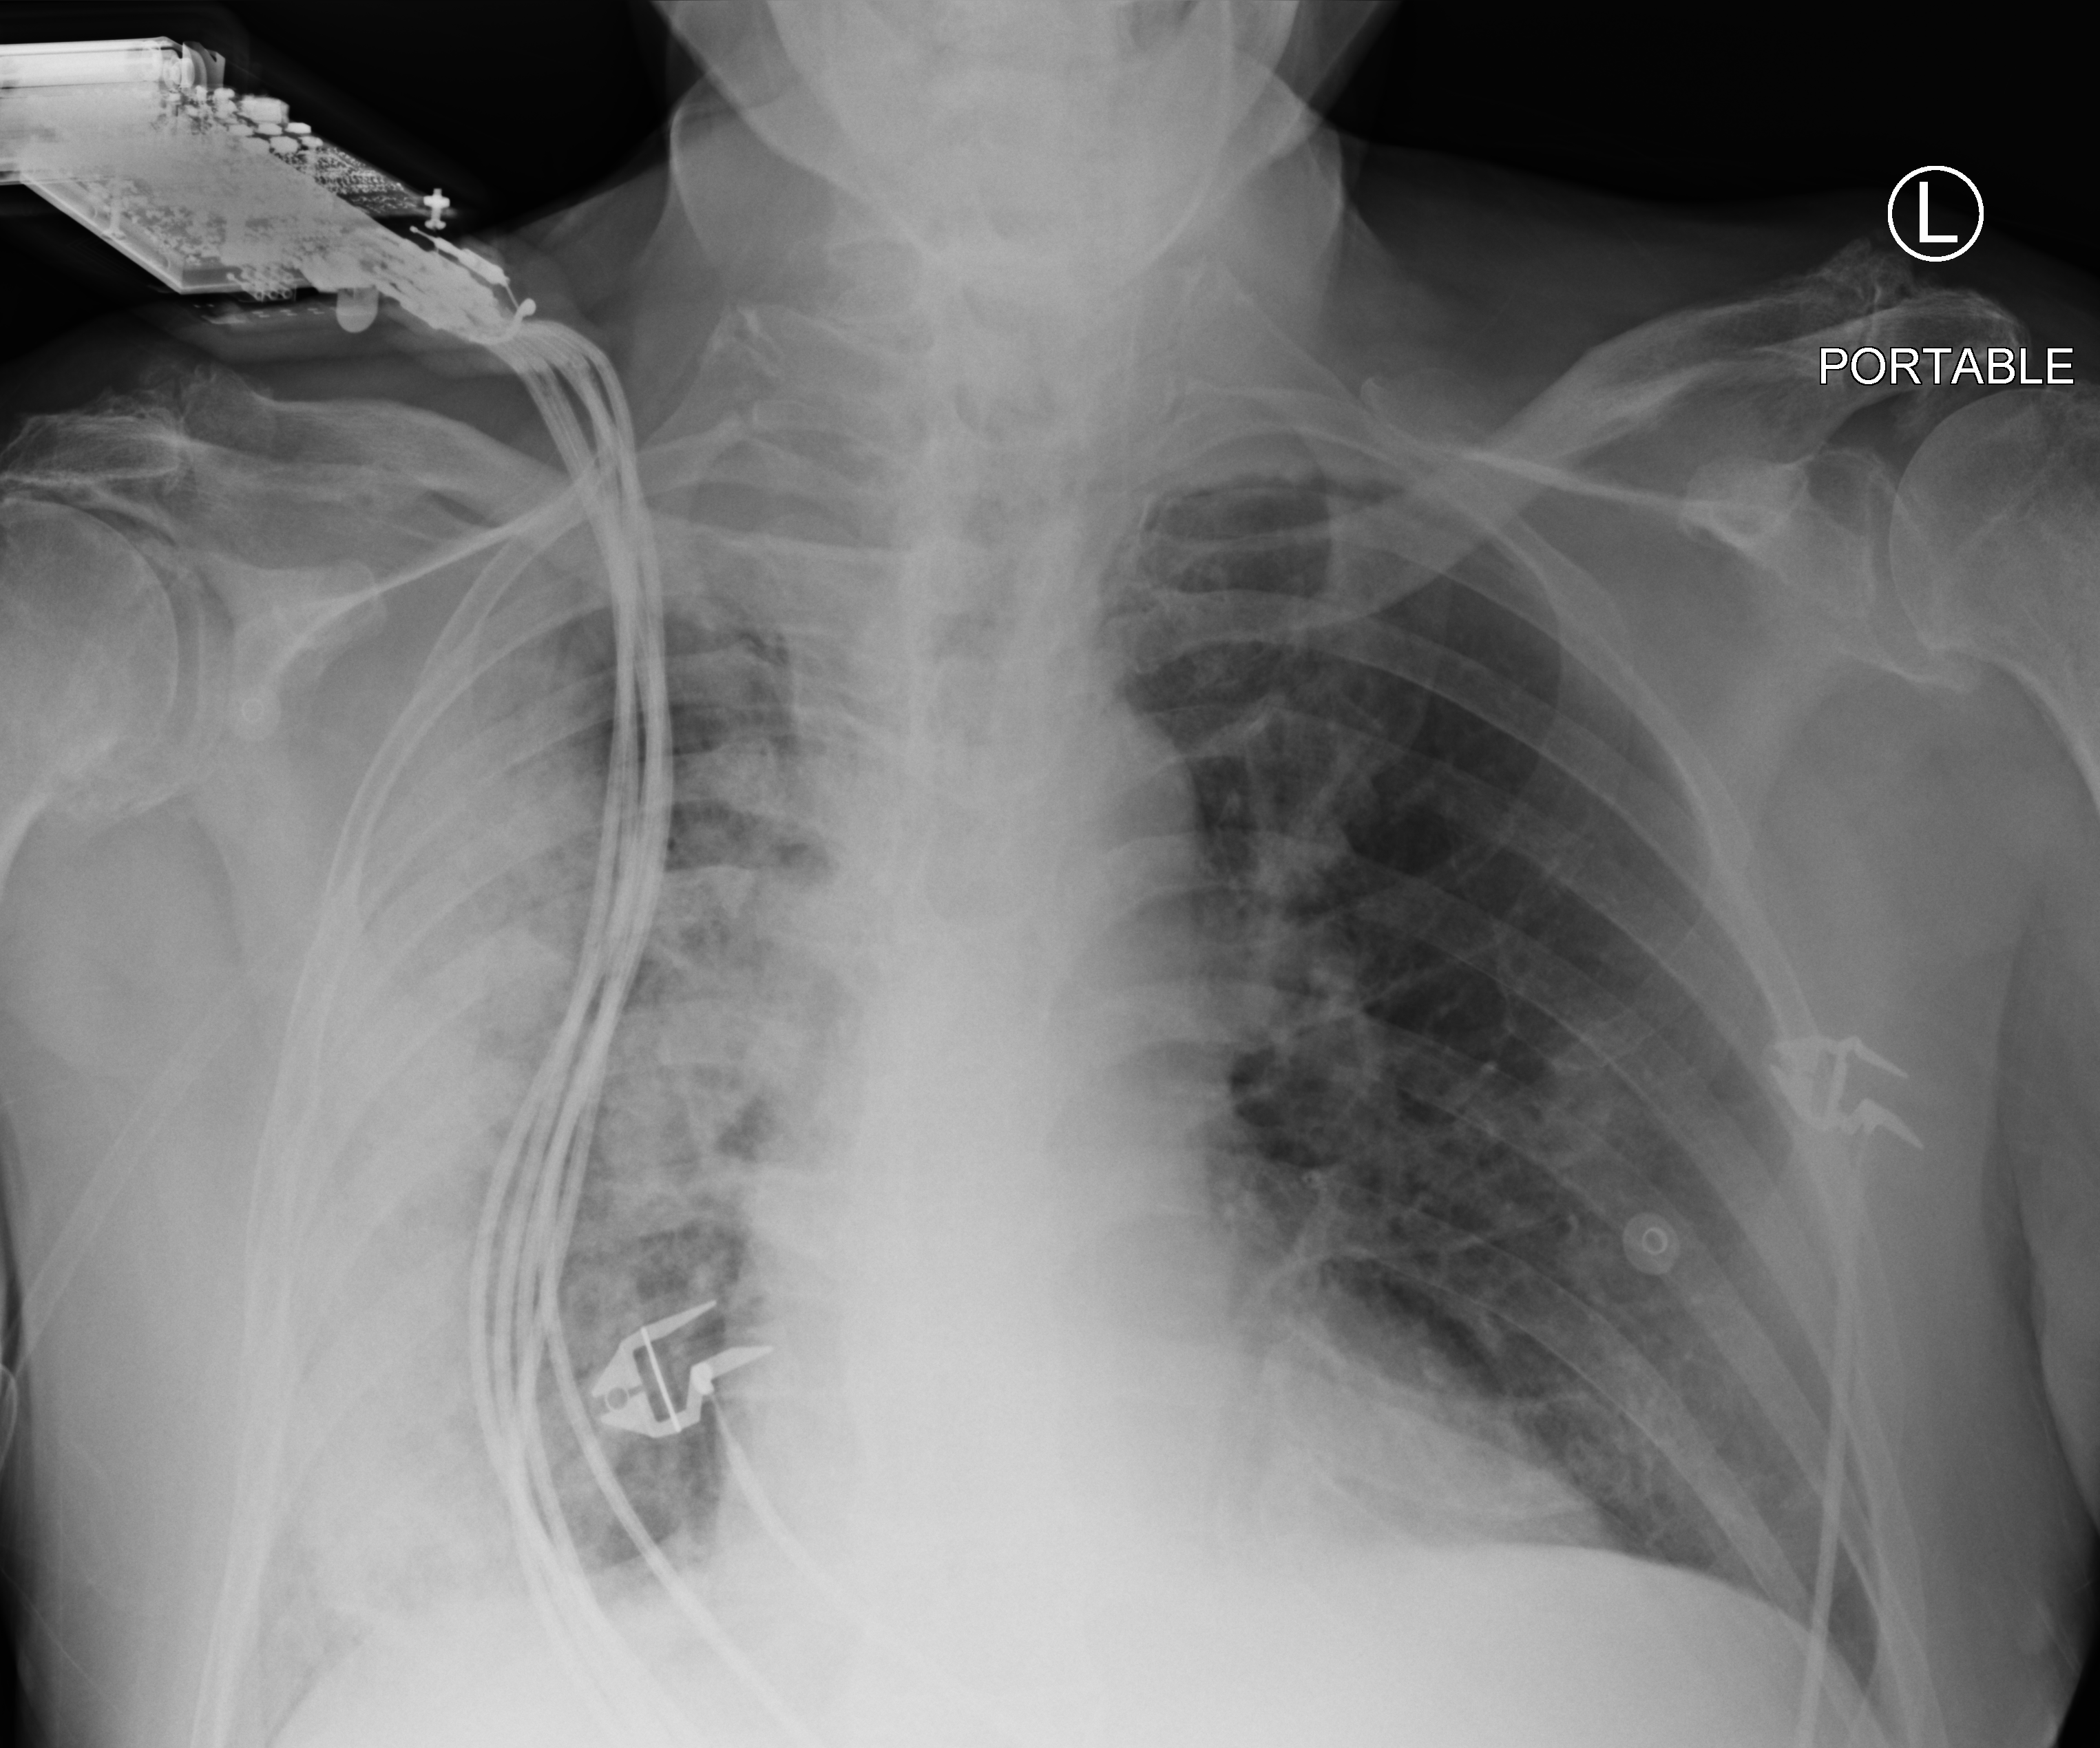
Portable chest radiograph; anteroposterior (AP) projection. Male patient hospitalised with COVID-19, age 75–90 years.
From the hospital-stay record, not from the radiograph (when in the stay this image was taken is not recorded): admitted to intensive care during this hospital stay: no.